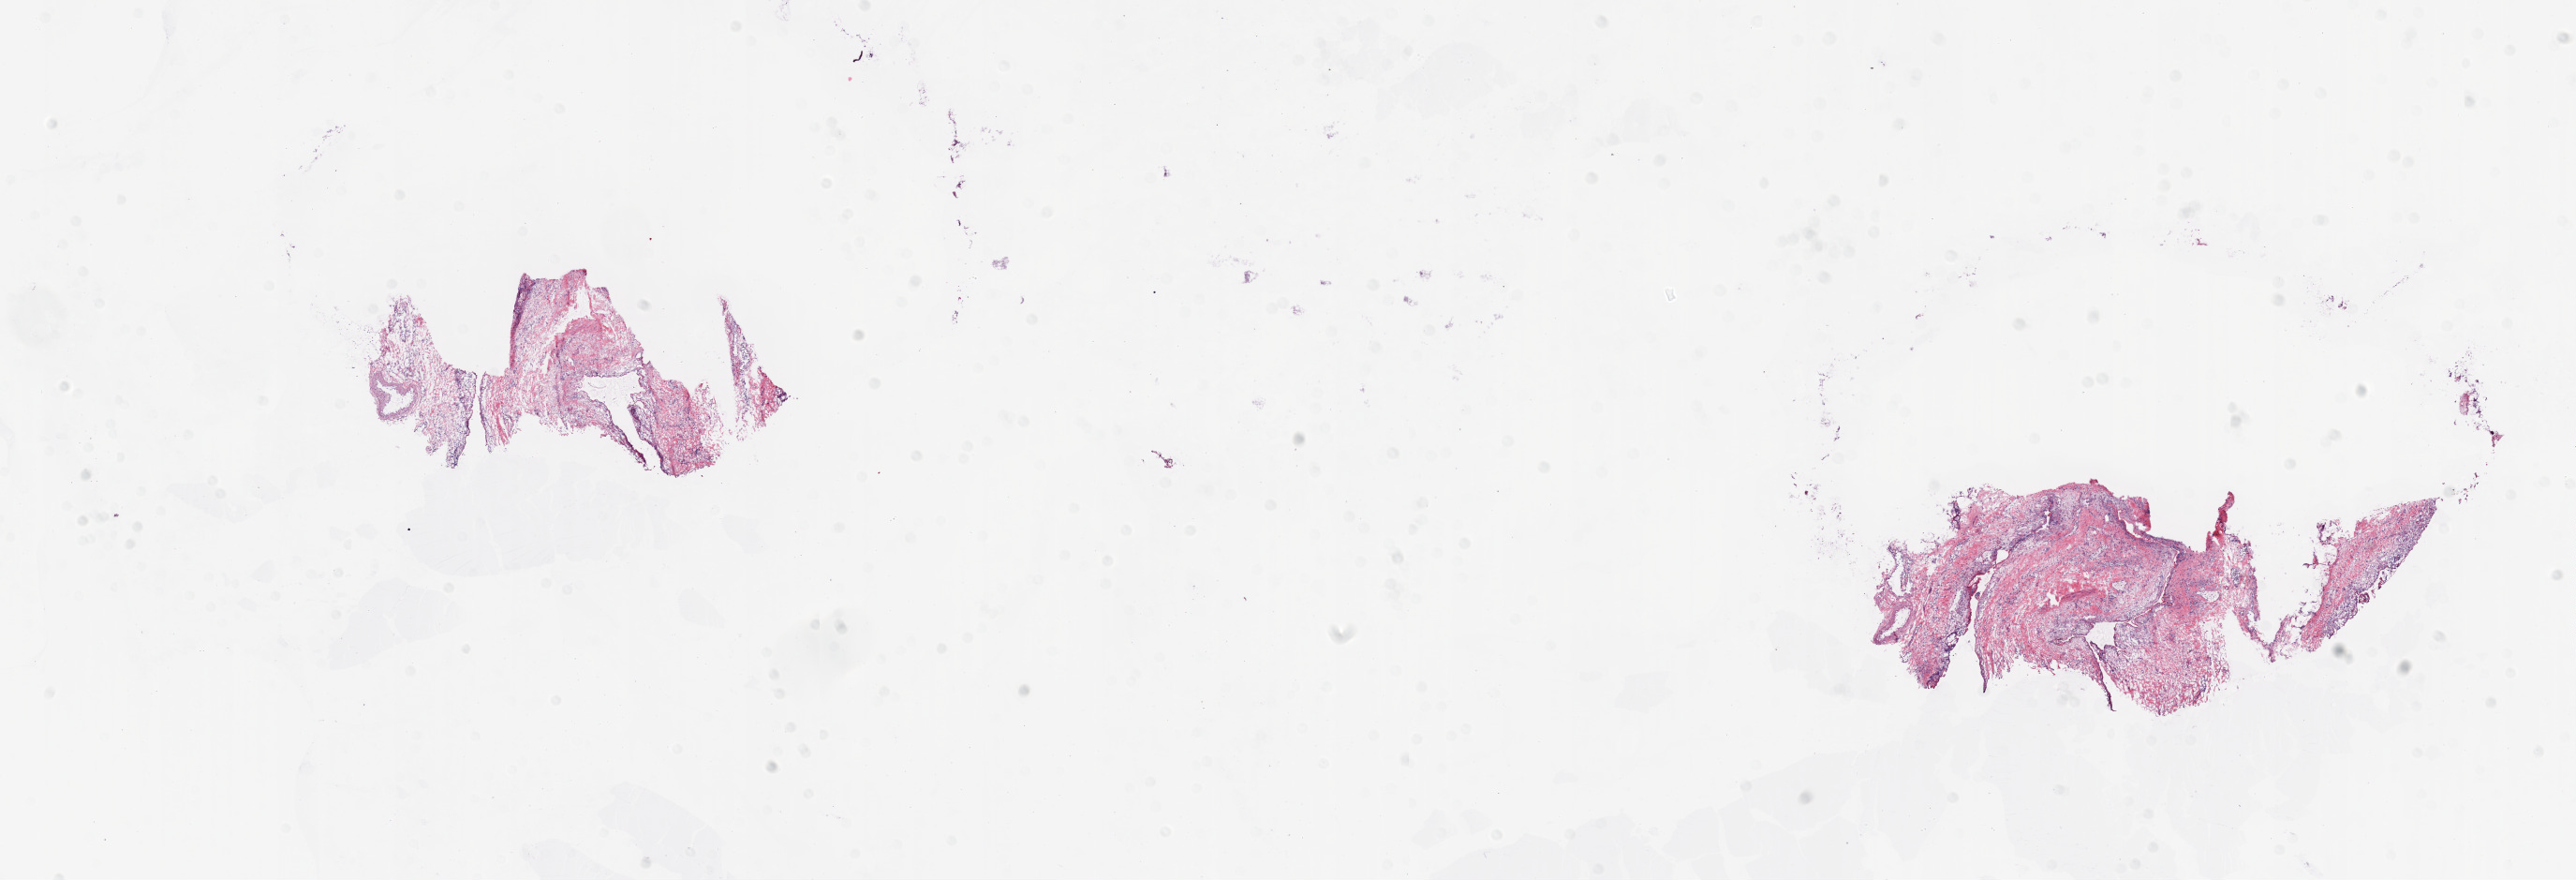
Whole-slide histology image, H&E-stained, whole scanned area (about 22.1 x 7.5 mm, from a 20x scan) shown as a low-resolution overview. Frozen section from the bottom of the tissue portion. Solid tissue normal (non-tumour tissue) sample from the ovary. Female, age 50 years at initial diagnosis.
- this section: solid tissue normal sample (biorepository sample class)
- patient diagnosis: Serous cystadenocarcinoma, NOS